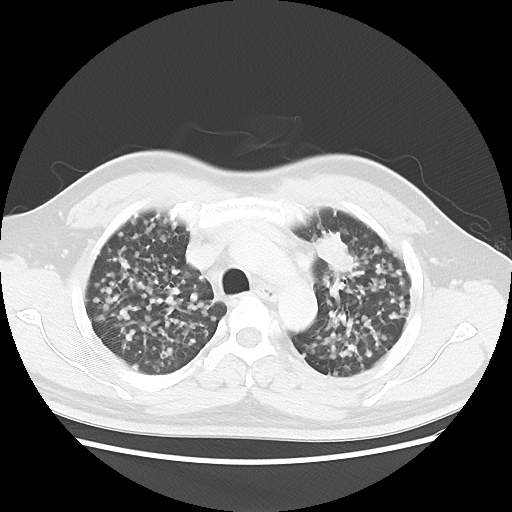
Chest CT, one axial slice; position 29 of 40 along the scan axis; reconstruction kernel LUNG; 120 kVp; lung window (W 1500 / L -600 HU); 5 mm slice thickness; 512 × 512 image matrix, field of view 366 × 366 mm. Patient: male, 41 years. Case-level facts recorded for this patient, not image findings: clinical TNM (as recorded): T1c N3 M1b.
Annotated regions visible in this slice (rectangle marked by the reading radiologist):
- lung tumour (recorded histology: adenocarcinoma): bounding box <311,227,353,278> (left, top, right, bottom; pixels)